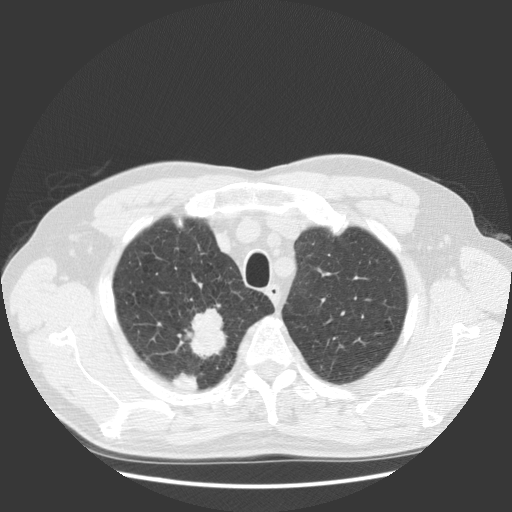
Axial slice from a low-dose chest CT screening exam; baseline annual screen; lung window (W 1500 / L -600 HU); 2.5 mm slice thickness; standard (soft-tissue) reconstruction kernel (STANDARD); 140 kVp; slice 106 of 131 in the series. Male participant, aged 63 years at enrolment. Current smoker at enrolment.
• Expert-annotated lung lesion, box from (x=165, y=316) to (x=236, y=382) px.
• The screening reader recorded 2 non-calcified nodules or masses ≥4 mm on this exam; which of them this box marks is not recorded.
• Official screen result: positive, change unspecified: nodule(s) >= 4 mm or enlarging nodule(s), mass(es), or other non-specific abnormalities suspicious for lung cancer.
• Later outcome: lung cancer diagnosed 30 days after this screen — squamous cell carcinoma, NOS, right upper lobe, stage IIIB (AJCC 6th edition), 35 mm at pathology.